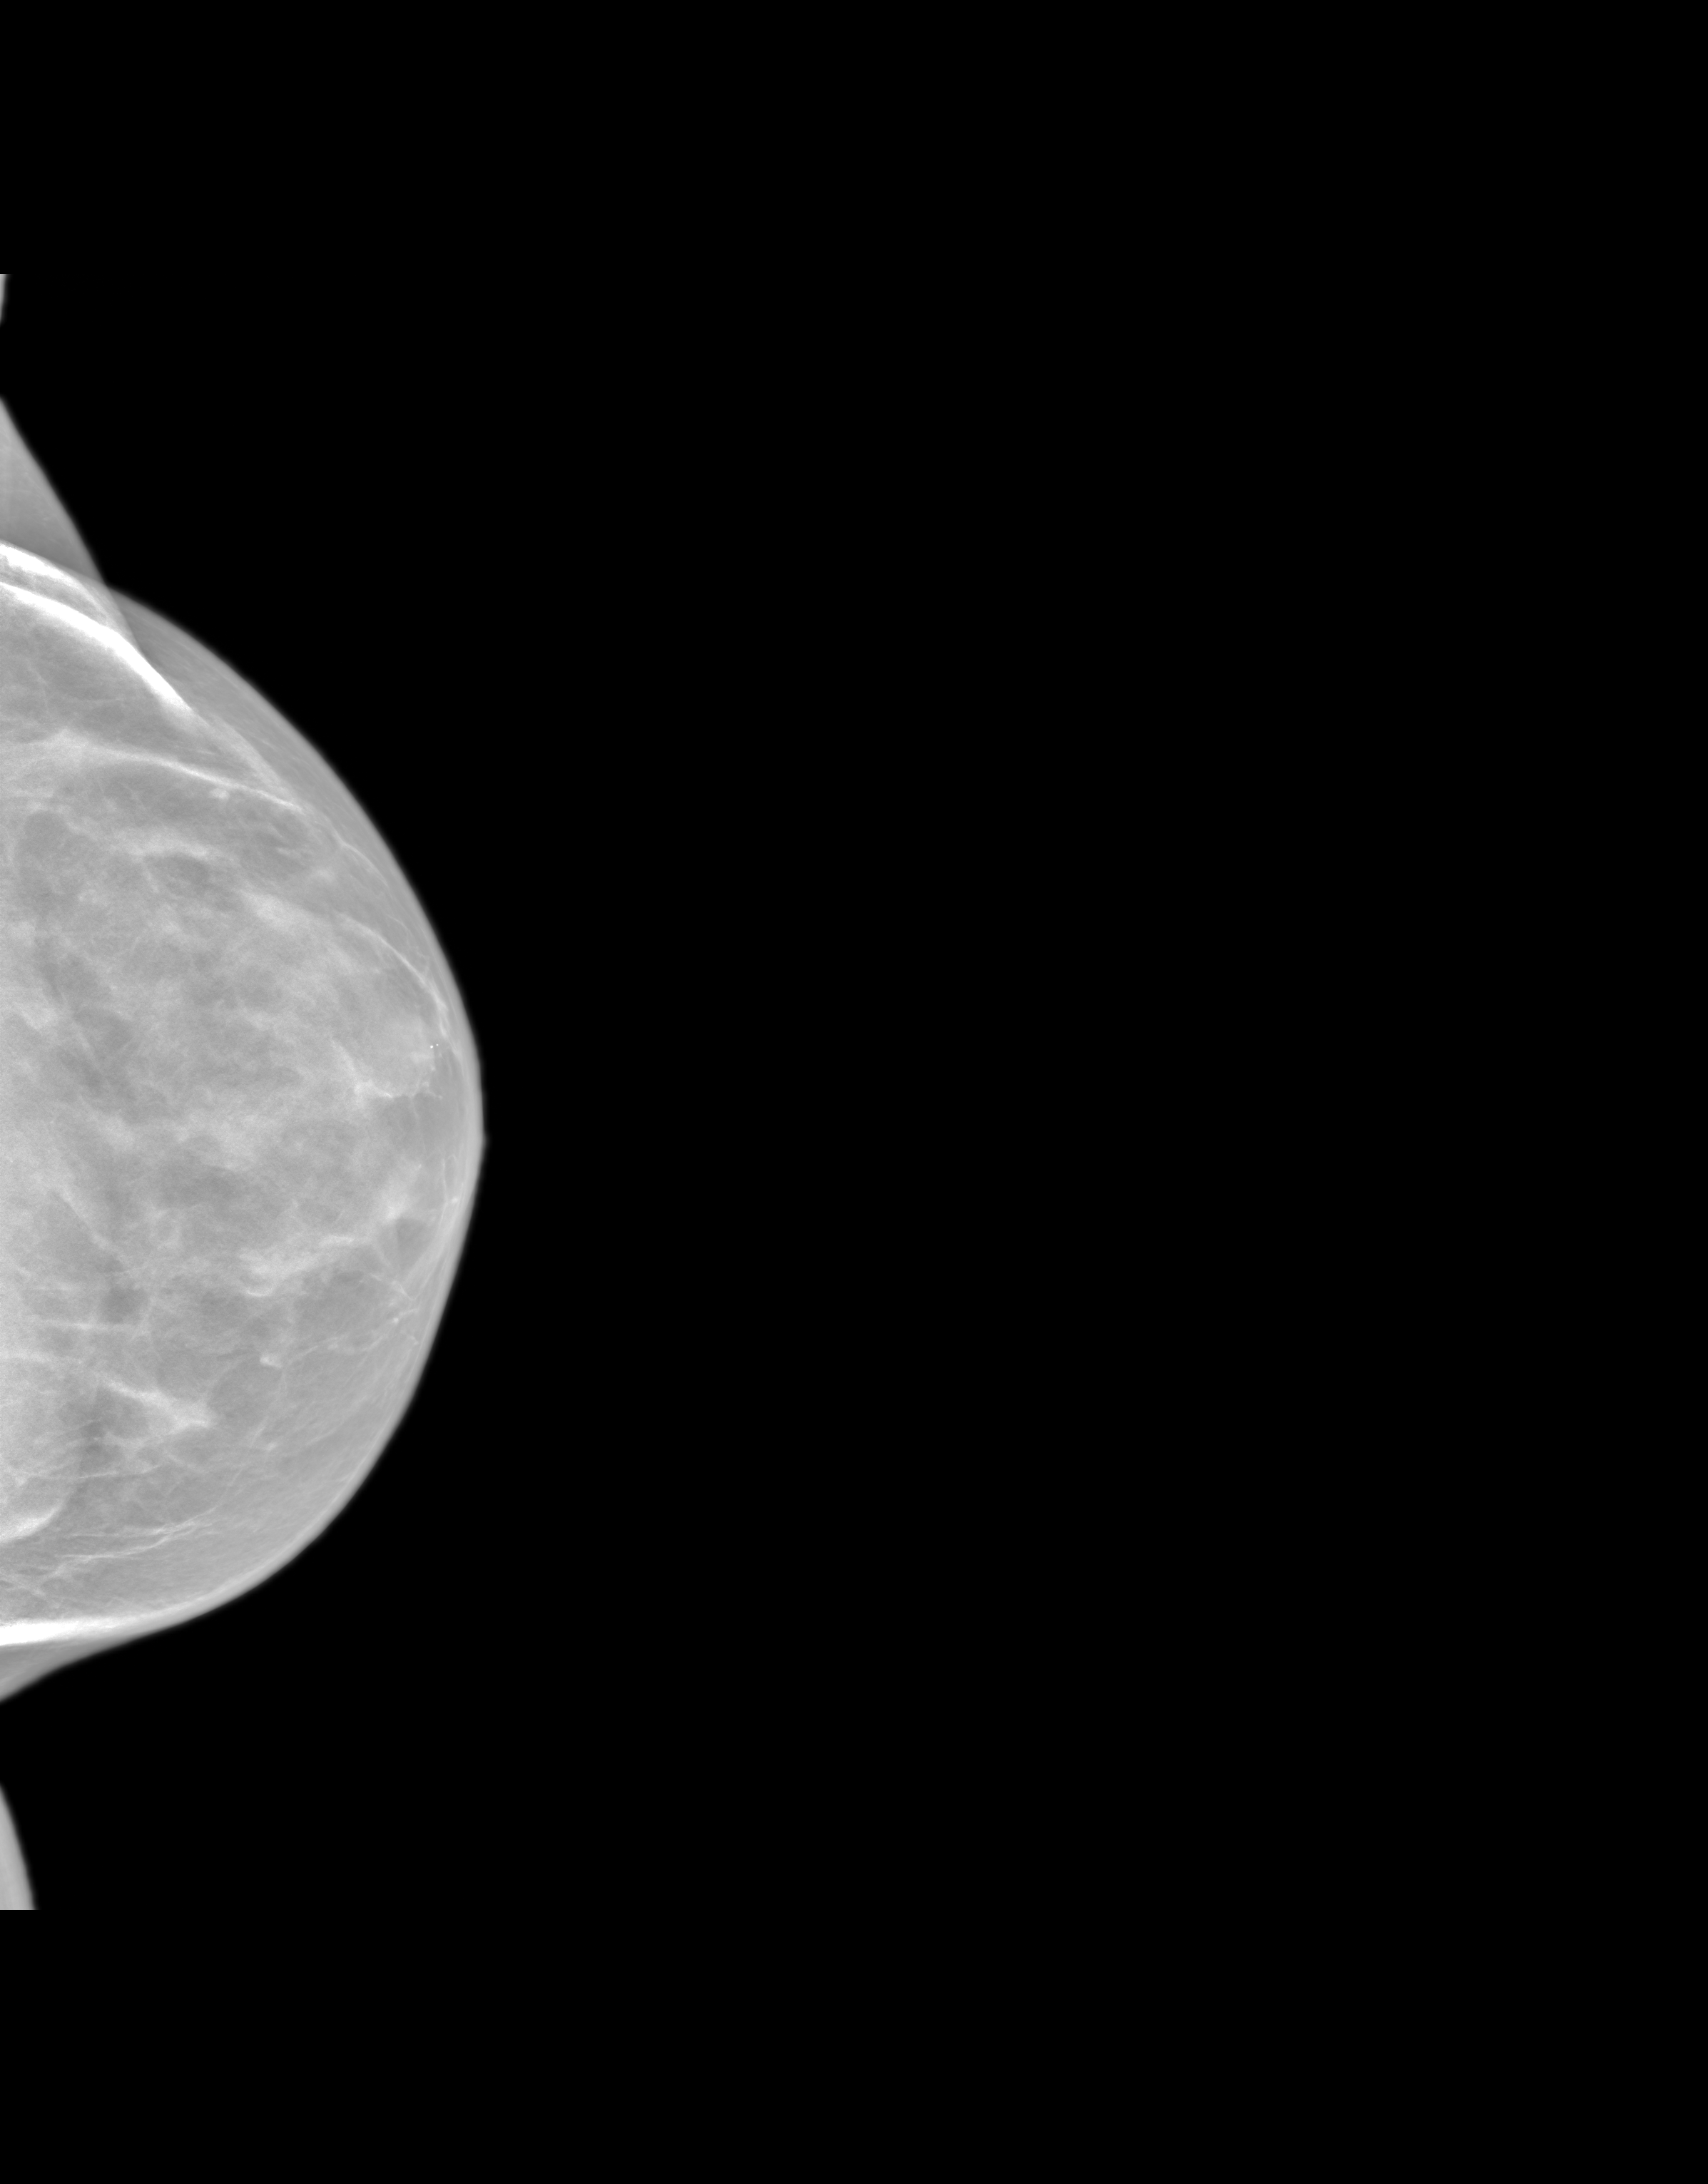
Synthesized 2-D mammogram reconstructed from digital breast tomosynthesis, left breast, craniocaudal (CC) view, screening examination, system: SenoIris_1SP1.1(421). Patient aged 66 years (female).
Breast density at the screening exam (both breasts): heterogeneously dense (BI-RADS density category c). Final BI-RADS assessment for this screening round (tomosynthesis exam, both breasts): category 1. Recall: no recall after this screen.